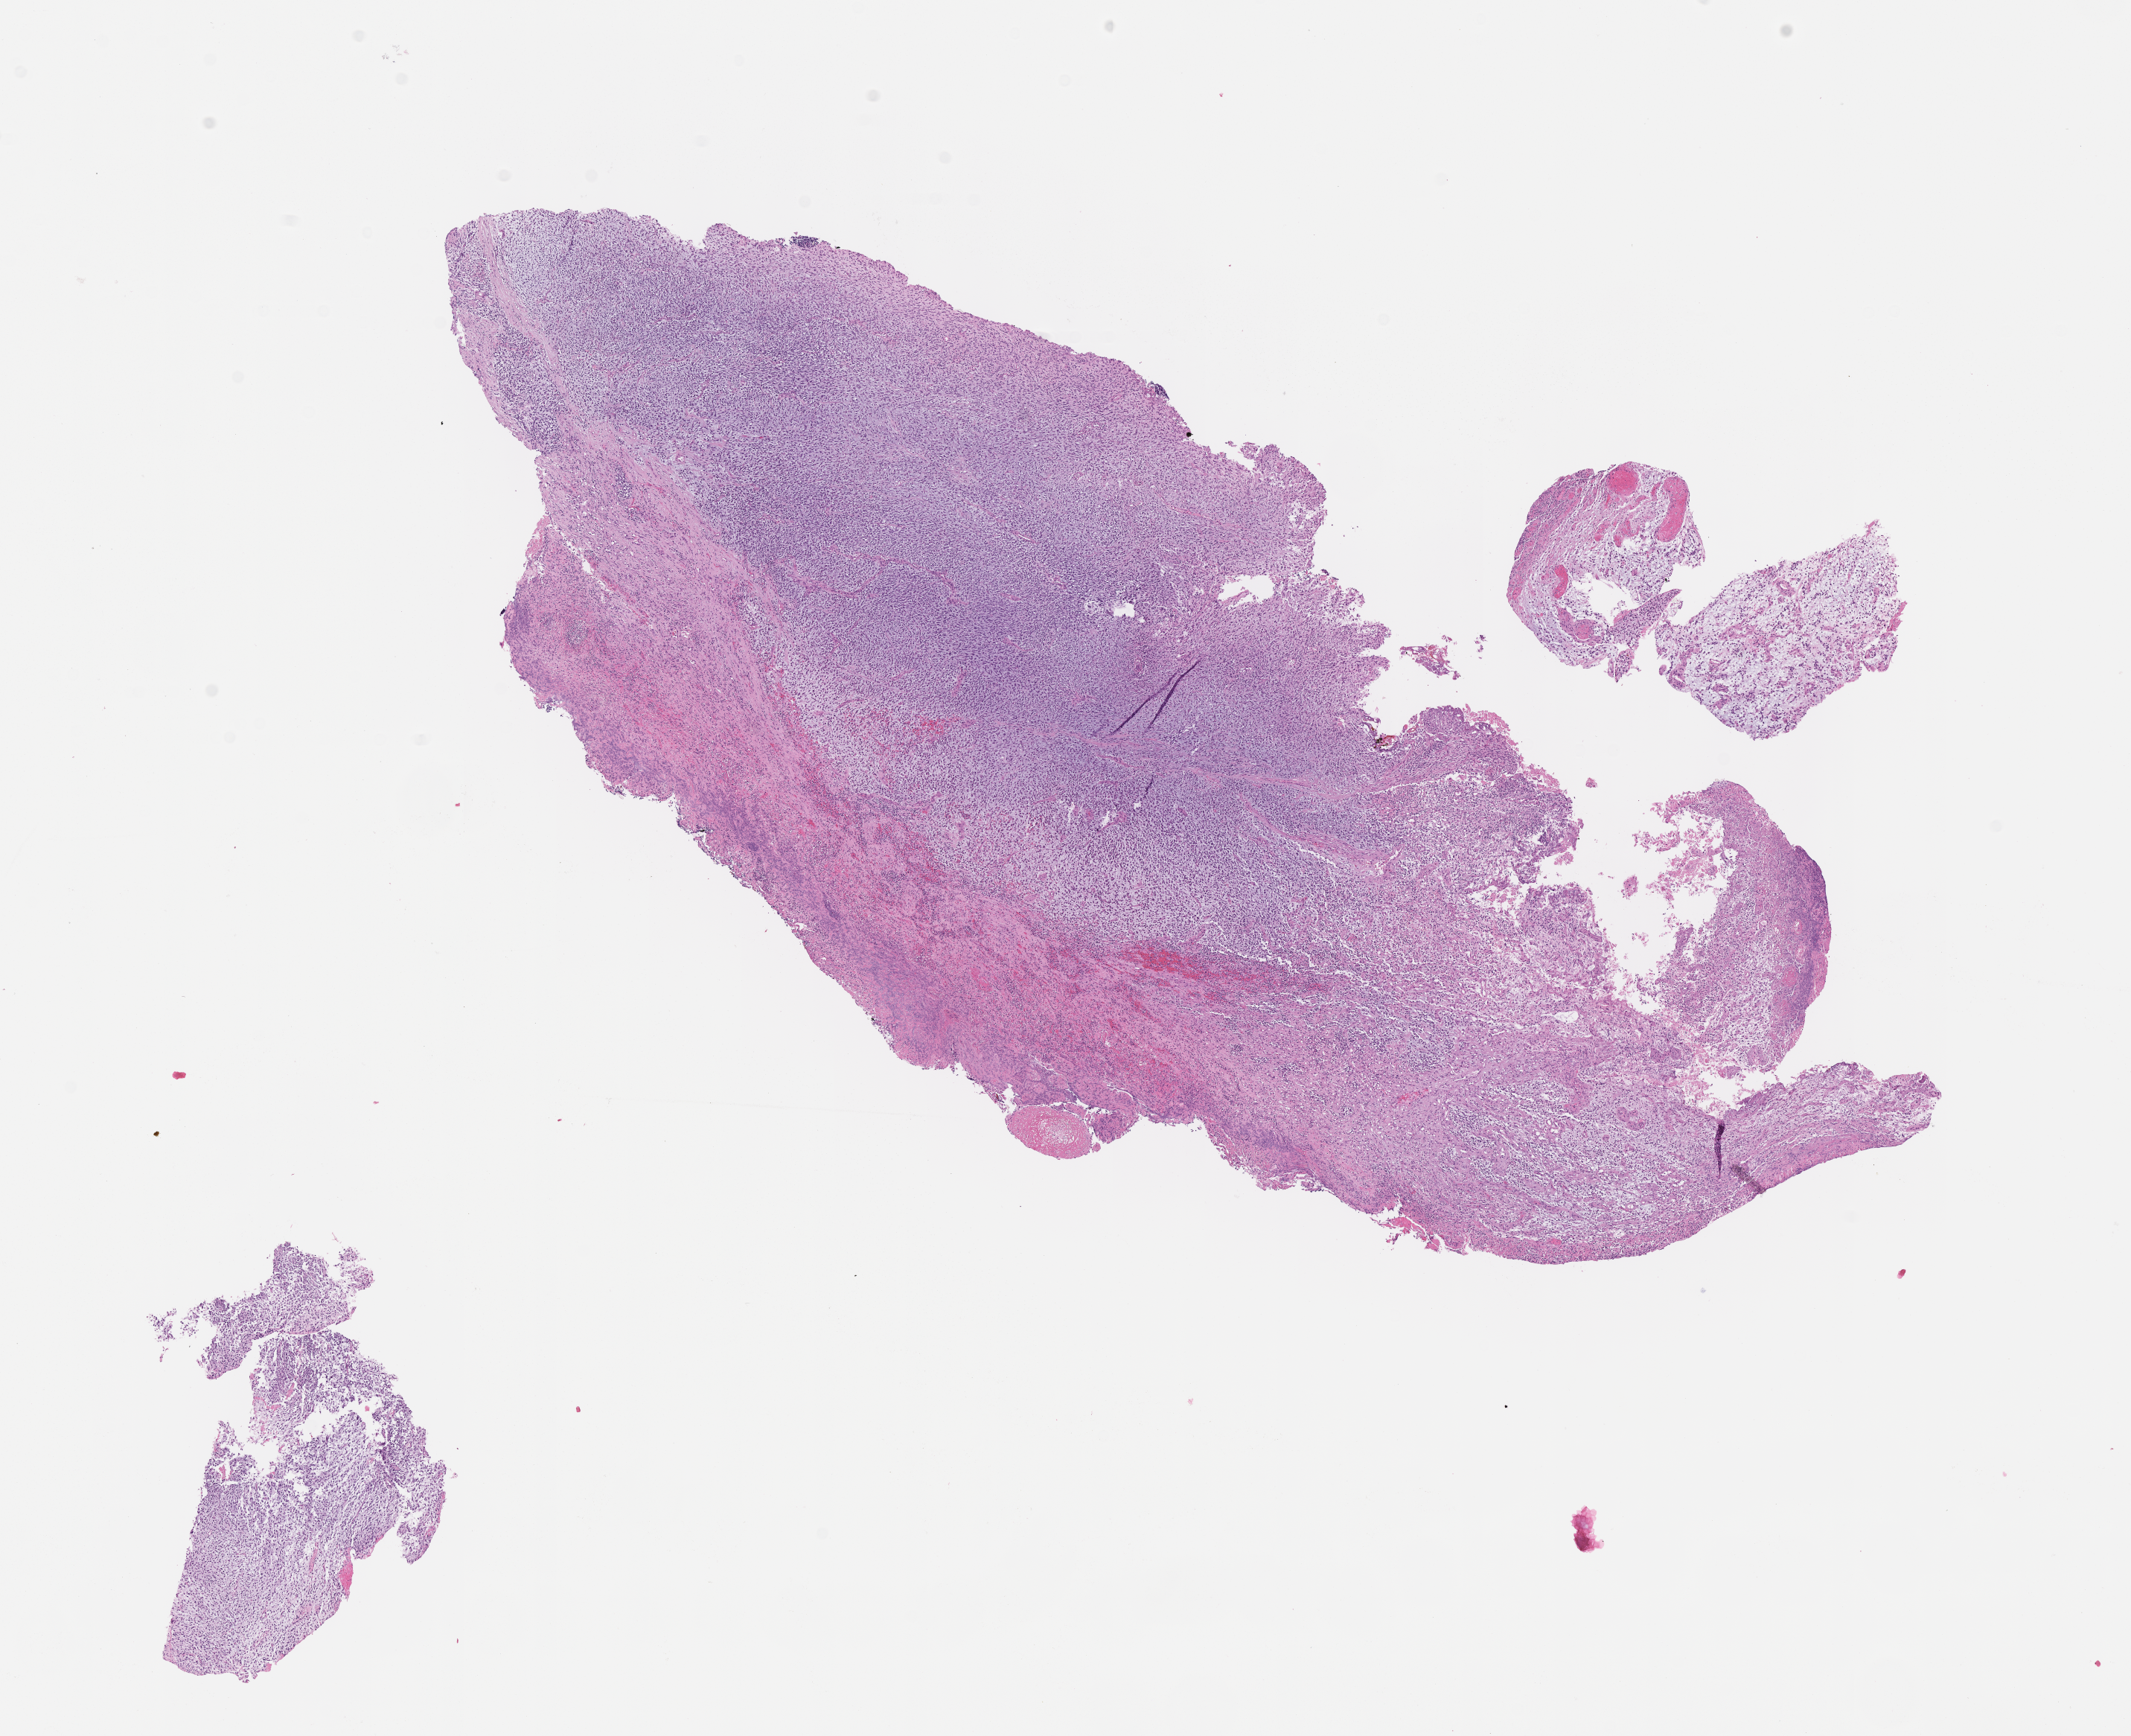
H&E whole-slide image of tumor tissue — whole scanned area (about 11.6 x 9.4 mm) shown as a low-resolution overview; formalin-fixed, paraffin-embedded (FFPE) tissue; site: nasopharynx. Male patient, age at diagnosis 5.3 years.
Diagnosis: rhabdomyosarcoma; histological classification: embryonal rhabdomyosarcoma.